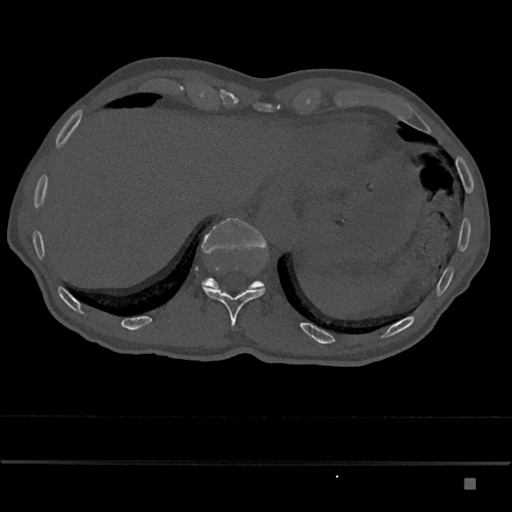
CT including the spine, one axial slice; position 657 of 797 along the scan axis; bone window (W 1800 / L 400 HU); 512 × 512 image matrix. Male patient, age 72 years. From the clinical record (not read from this slice): primary cancer: prostate.
Outlined on this slice (semi-automatically segmented with operator editing):
- T11 vertebra: bounding box (x1, y1, x2, y2) in pixels: (202, 283, 265, 326)
- T12 vertebra: (201, 218, 267, 289)